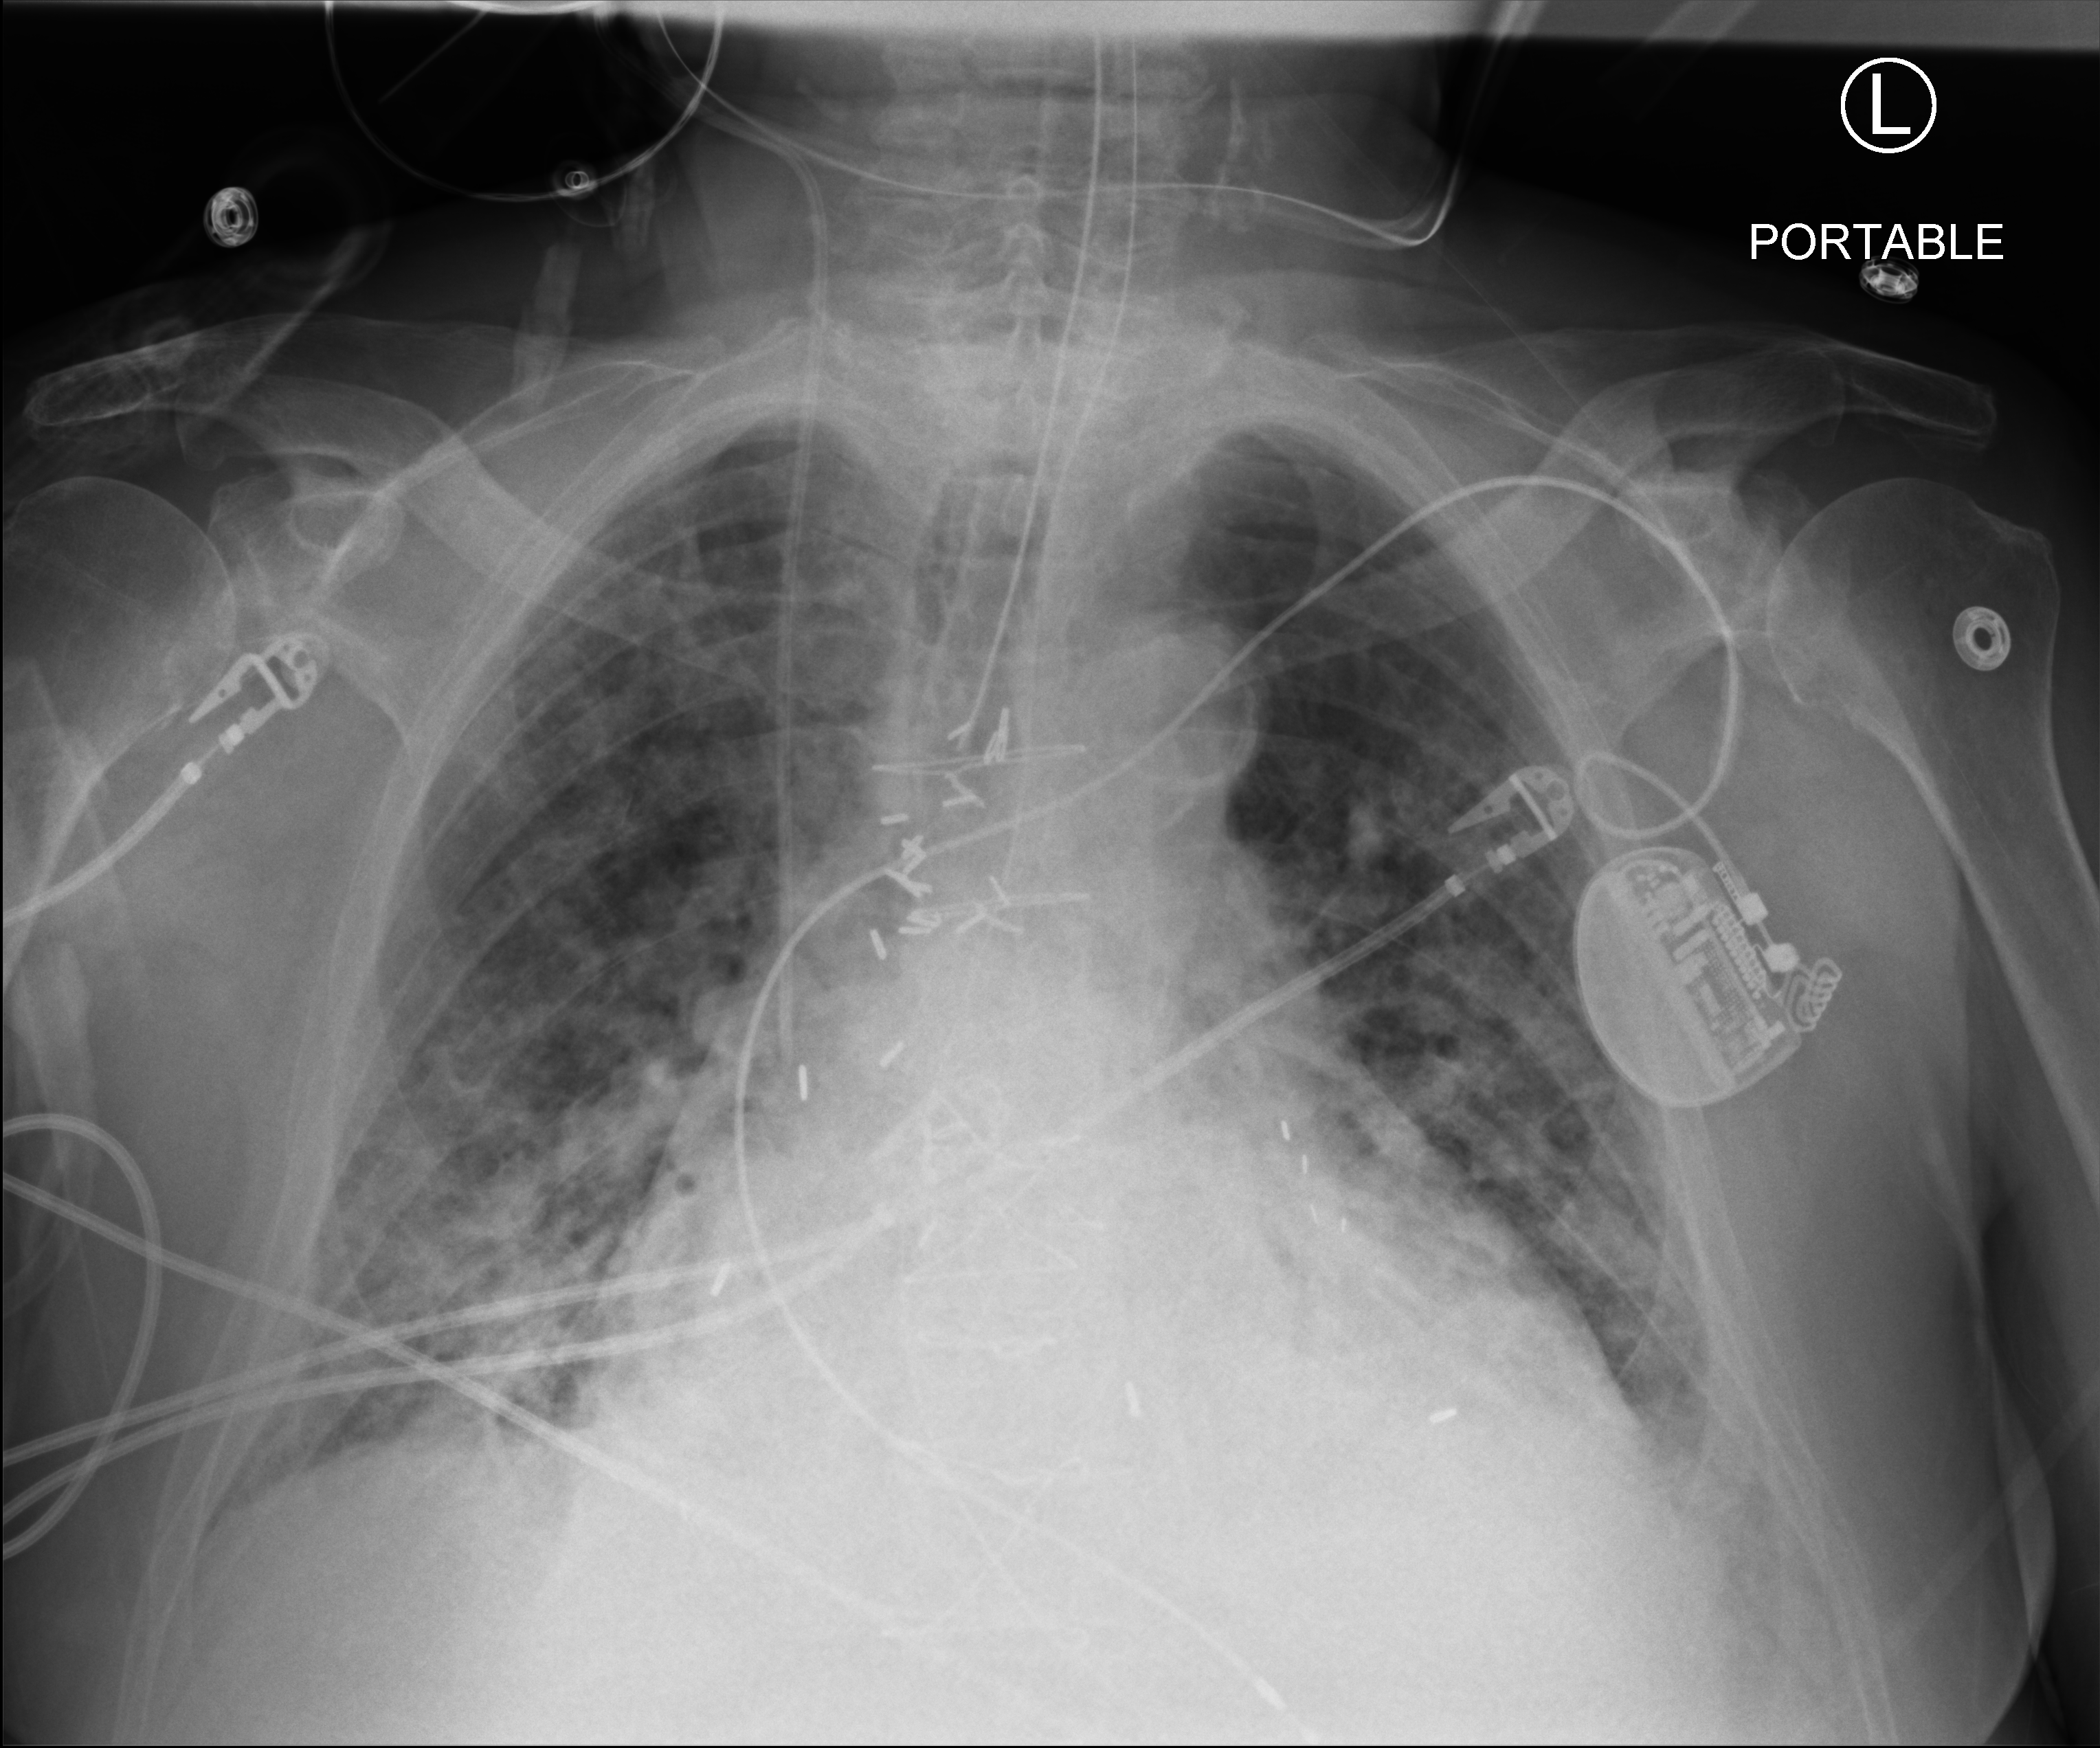
Chest X-ray (portable); anteroposterior (AP) projection. Male patient hospitalised with COVID-19, age 75–90 years.
Admission-level facts for this patient (not findings on this image; timing relative to this image not recorded):
- COPD (admission record): no
- admitted to intensive care during this hospital stay: yes
- mechanically ventilated during this hospital stay: yes